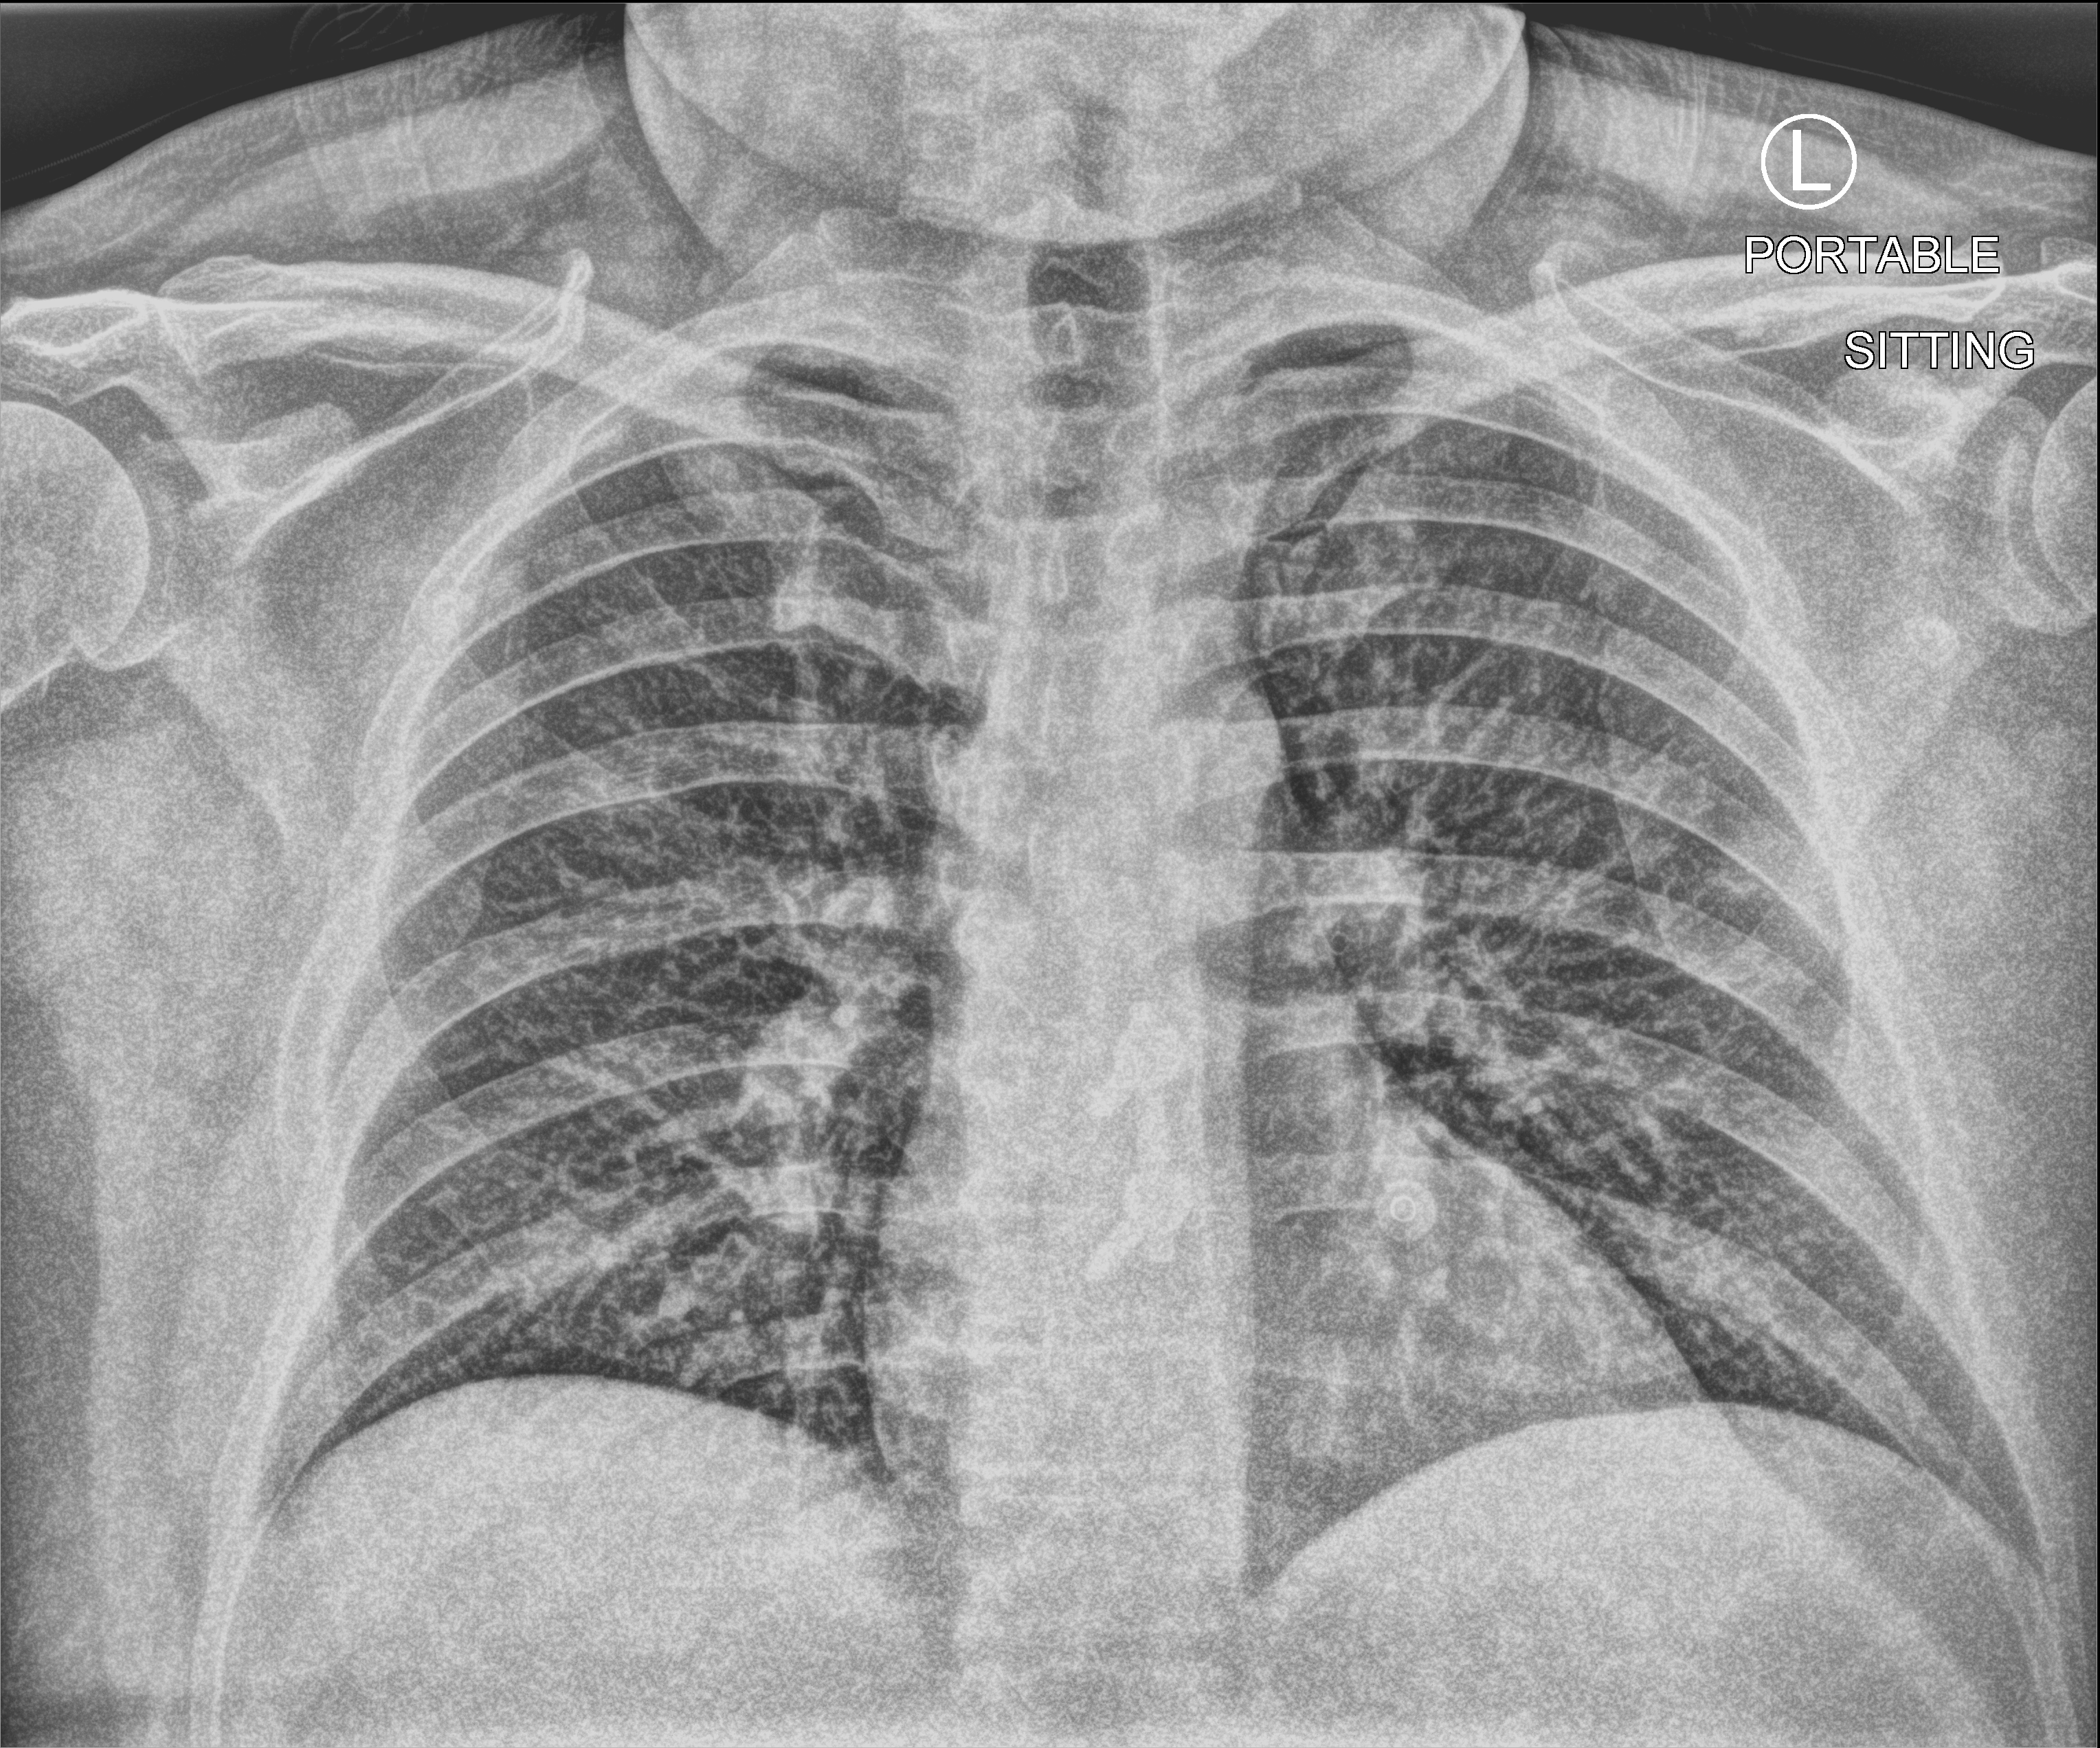
Portable chest radiograph. Male patient hospitalised with COVID-19, age 18–59 years.
Hospital-stay facts (about this admission, not read from this image; timing relative to this image not recorded):
- mechanically ventilated during this hospital stay: no